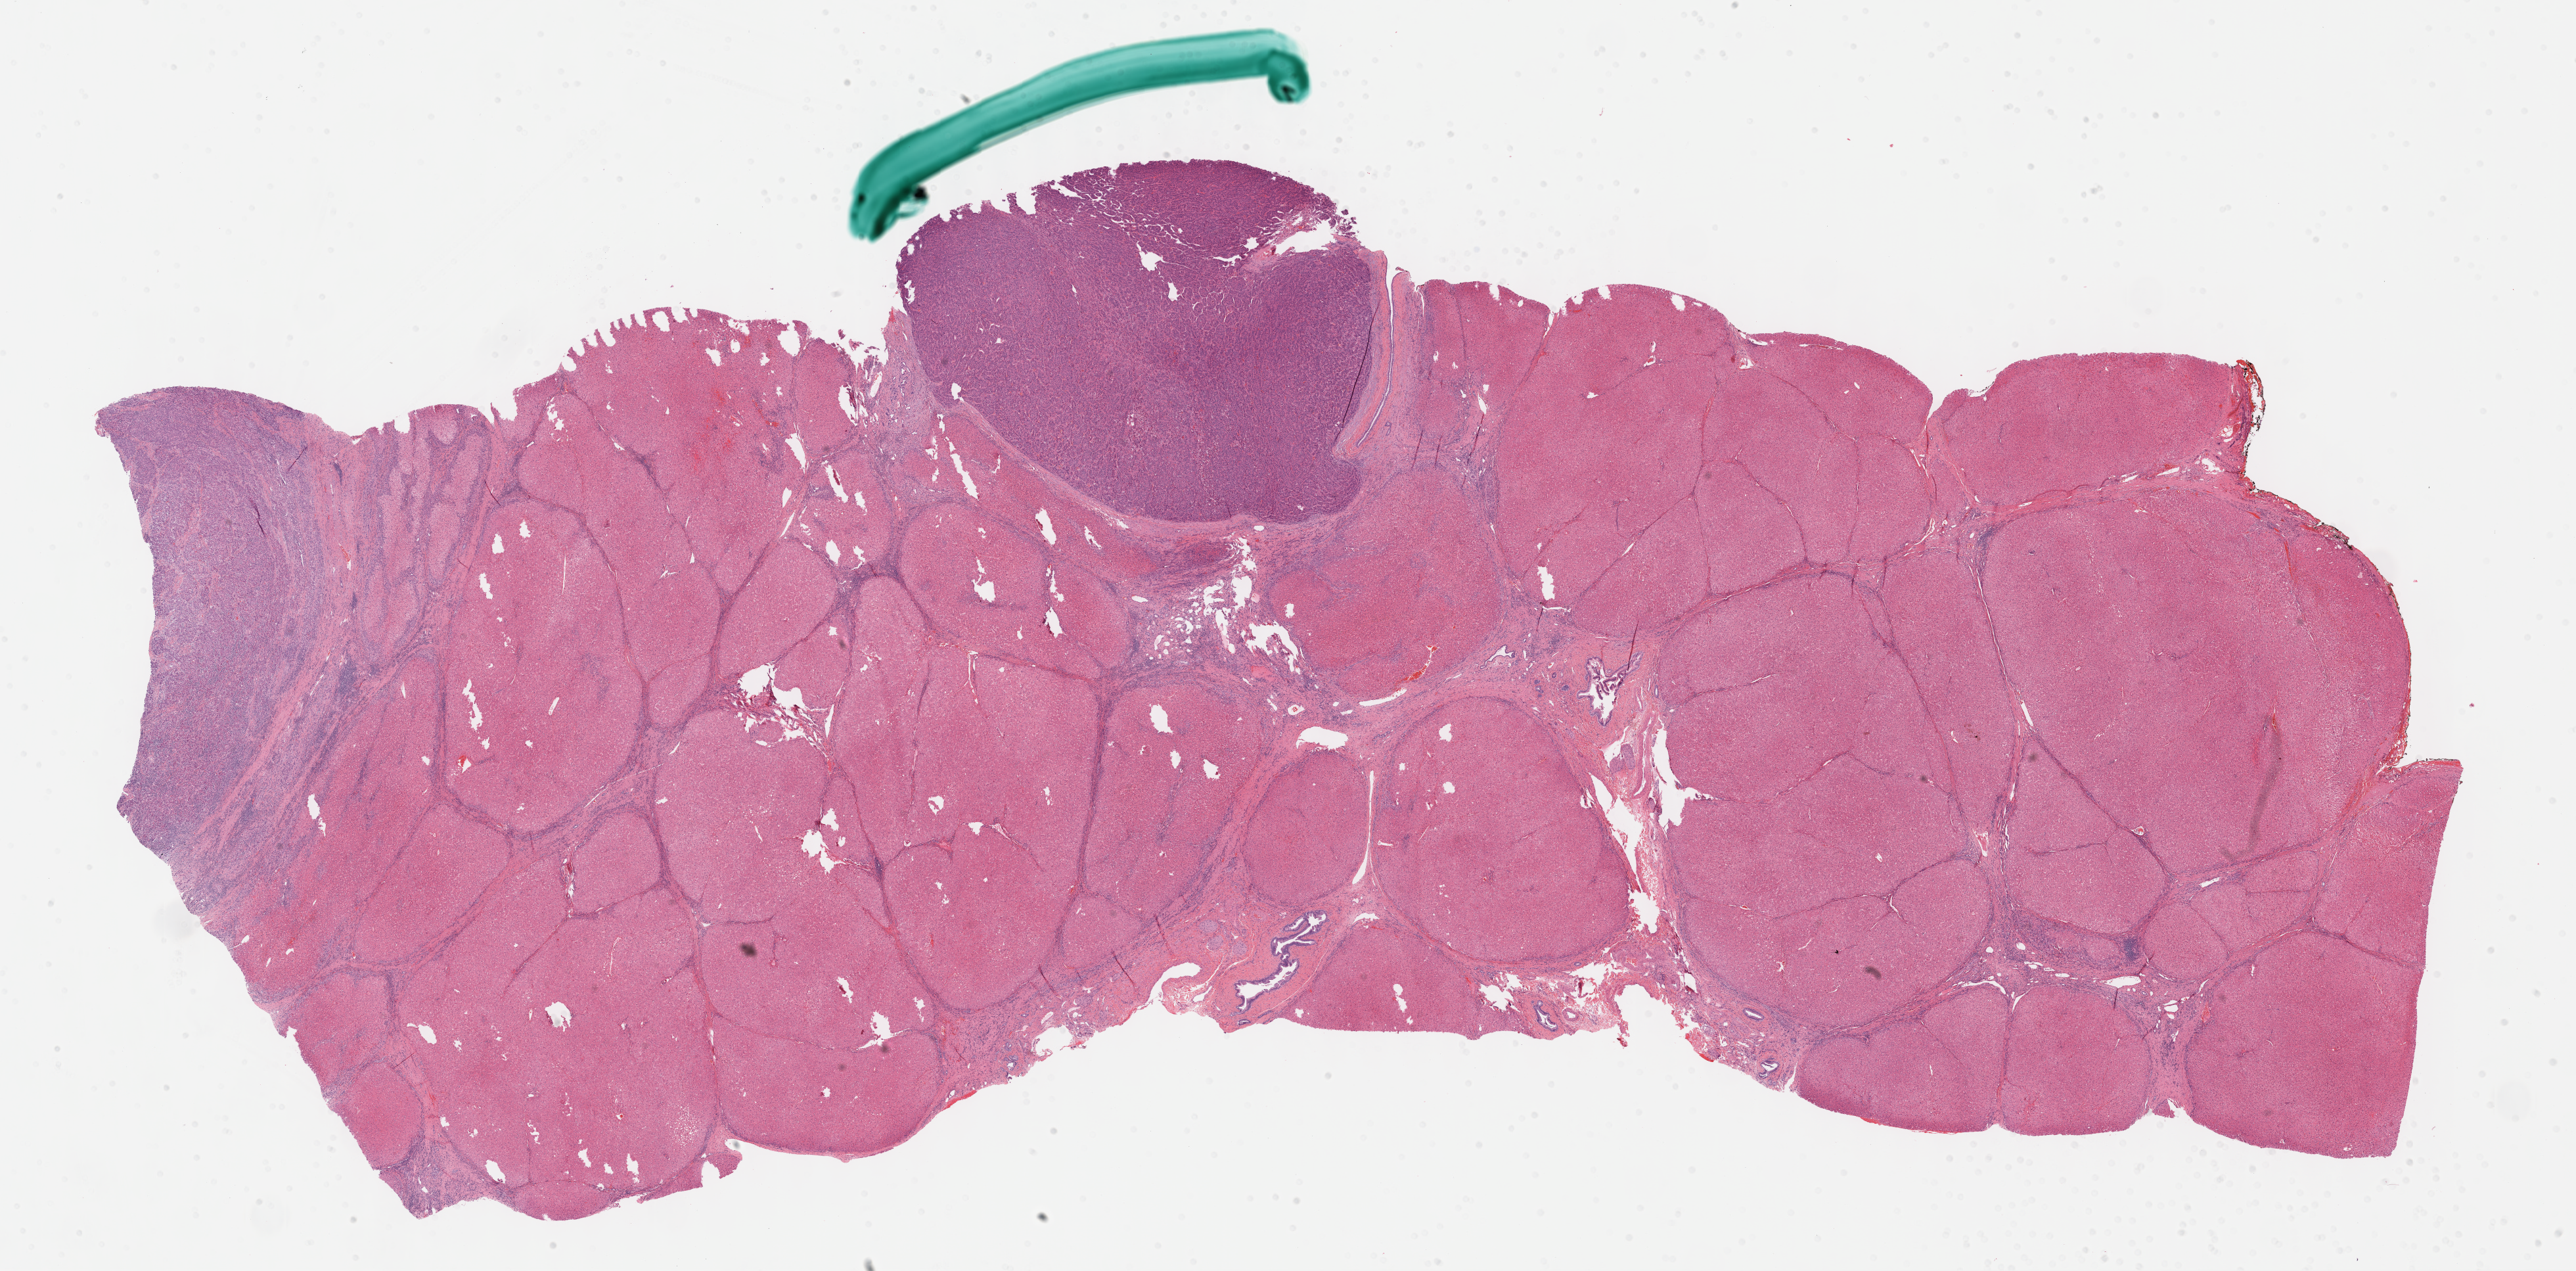
Hematoxylin and eosin (H&E) stained whole-slide image — low-resolution overview of the scanned area, about 31.7 x 15.6 mm, formalin-fixed paraffin-embedded (FFPE) diagnostic section, liver, primary tumour sample. Patient: male, age at initial diagnosis 56 years. Histologic grade: G2 (moderately differentiated).
• AJCC pathologic stage: IIIA (7th edition)
• pathologic diagnosis: Hepatocellular carcinoma, NOS